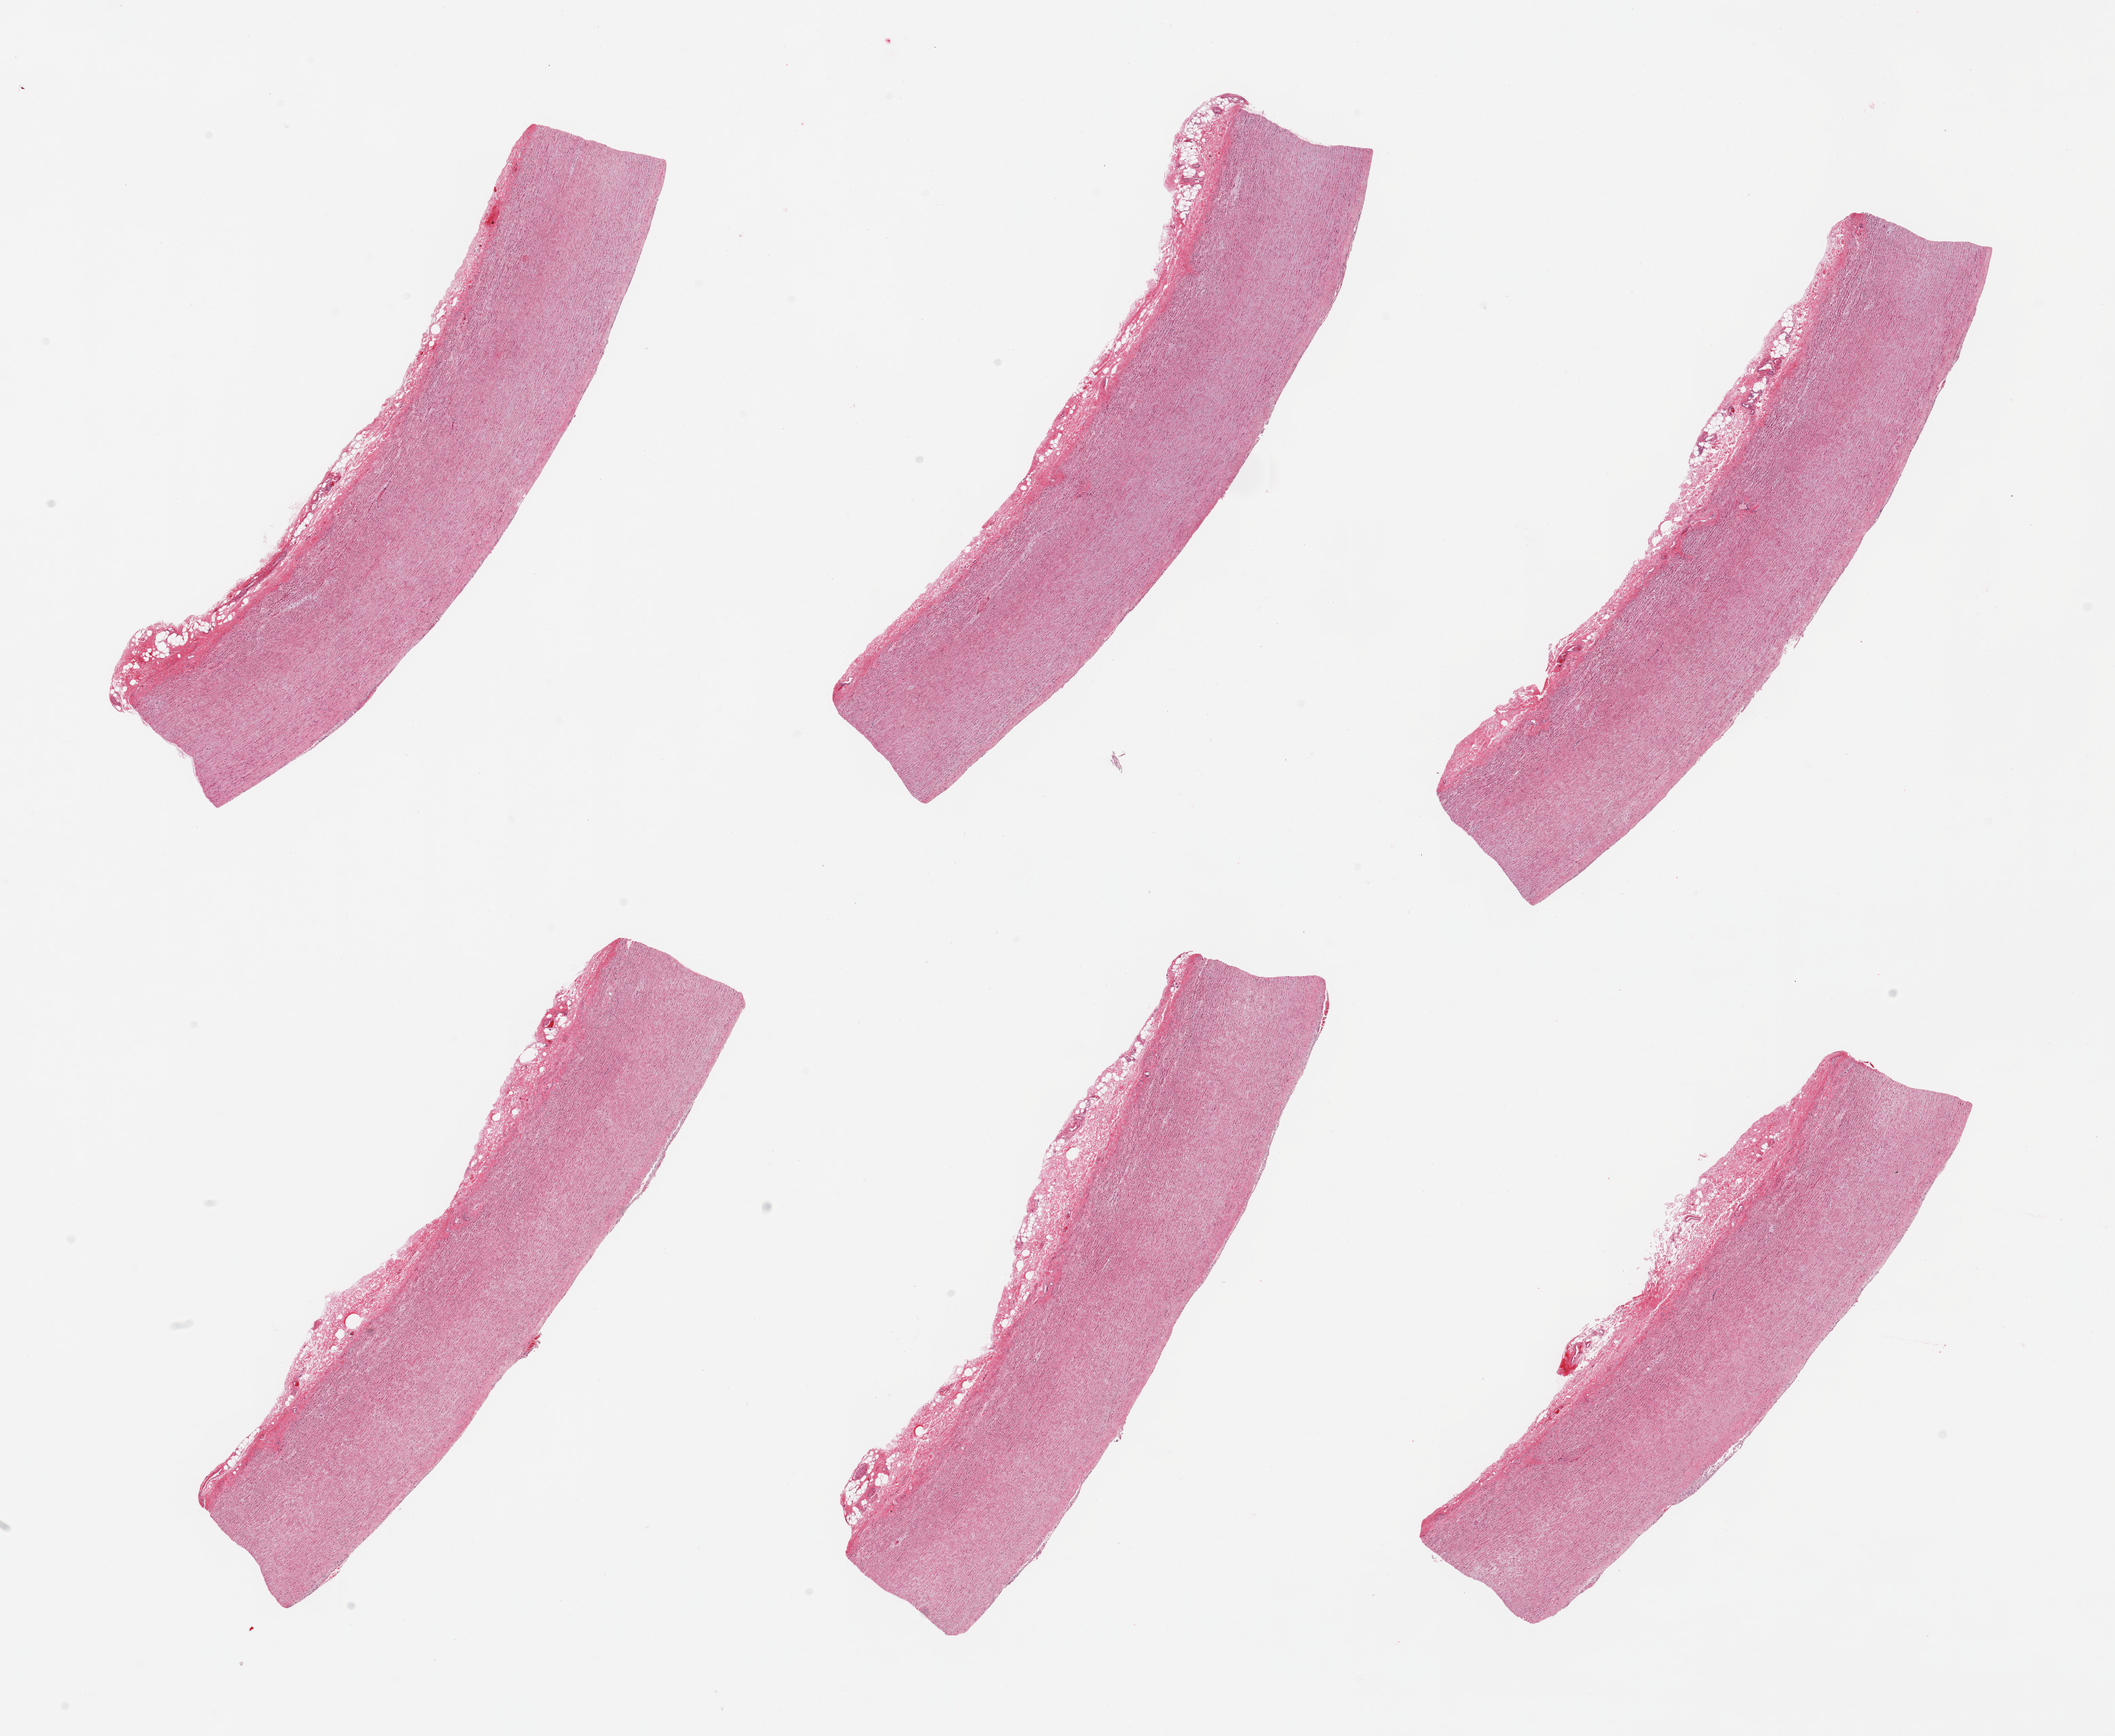
Digitized H&E-stained section — whole scanned area (about 24.6 x 20.2 mm, acquisition: 20x scan) shown as a low-resolution overview. PAXgene-fixed paraffin-embedded (PFPE) section. Section of aorta (target tissue). Tissue donor sample. Donor: female.
Review note (as recorded): 6 pieces; well trimmed; no plaques.